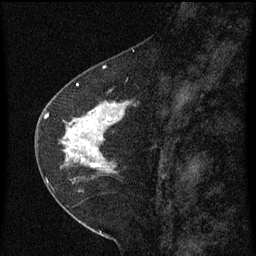
Breast MRI (dynamic contrast-enhanced), one sagittal slice; position 29 of 60 along the scan axis; dynamic contrast-enhanced series, image 2 of 3 at this slice position (ordered by acquisition); 1.5 T; TE 4.2 ms, TR 8 ms; 2 mm slice thickness; 256 × 256 image matrix. Female patient, age 47 years.
Outlined on this slice (semi-automatic segmentation, software-assisted and operator-edited):
- analysis volume of interest (the breast-tissue region the enhancement analysis was run in; not a lesion): bounding box (x1, y1, x2, y2) in pixels: (44, 84, 139, 199)
- tumour enhancement mask (voxels above the 70 % enhancement threshold inside the analysis volume of interest): (44, 84, 123, 183)